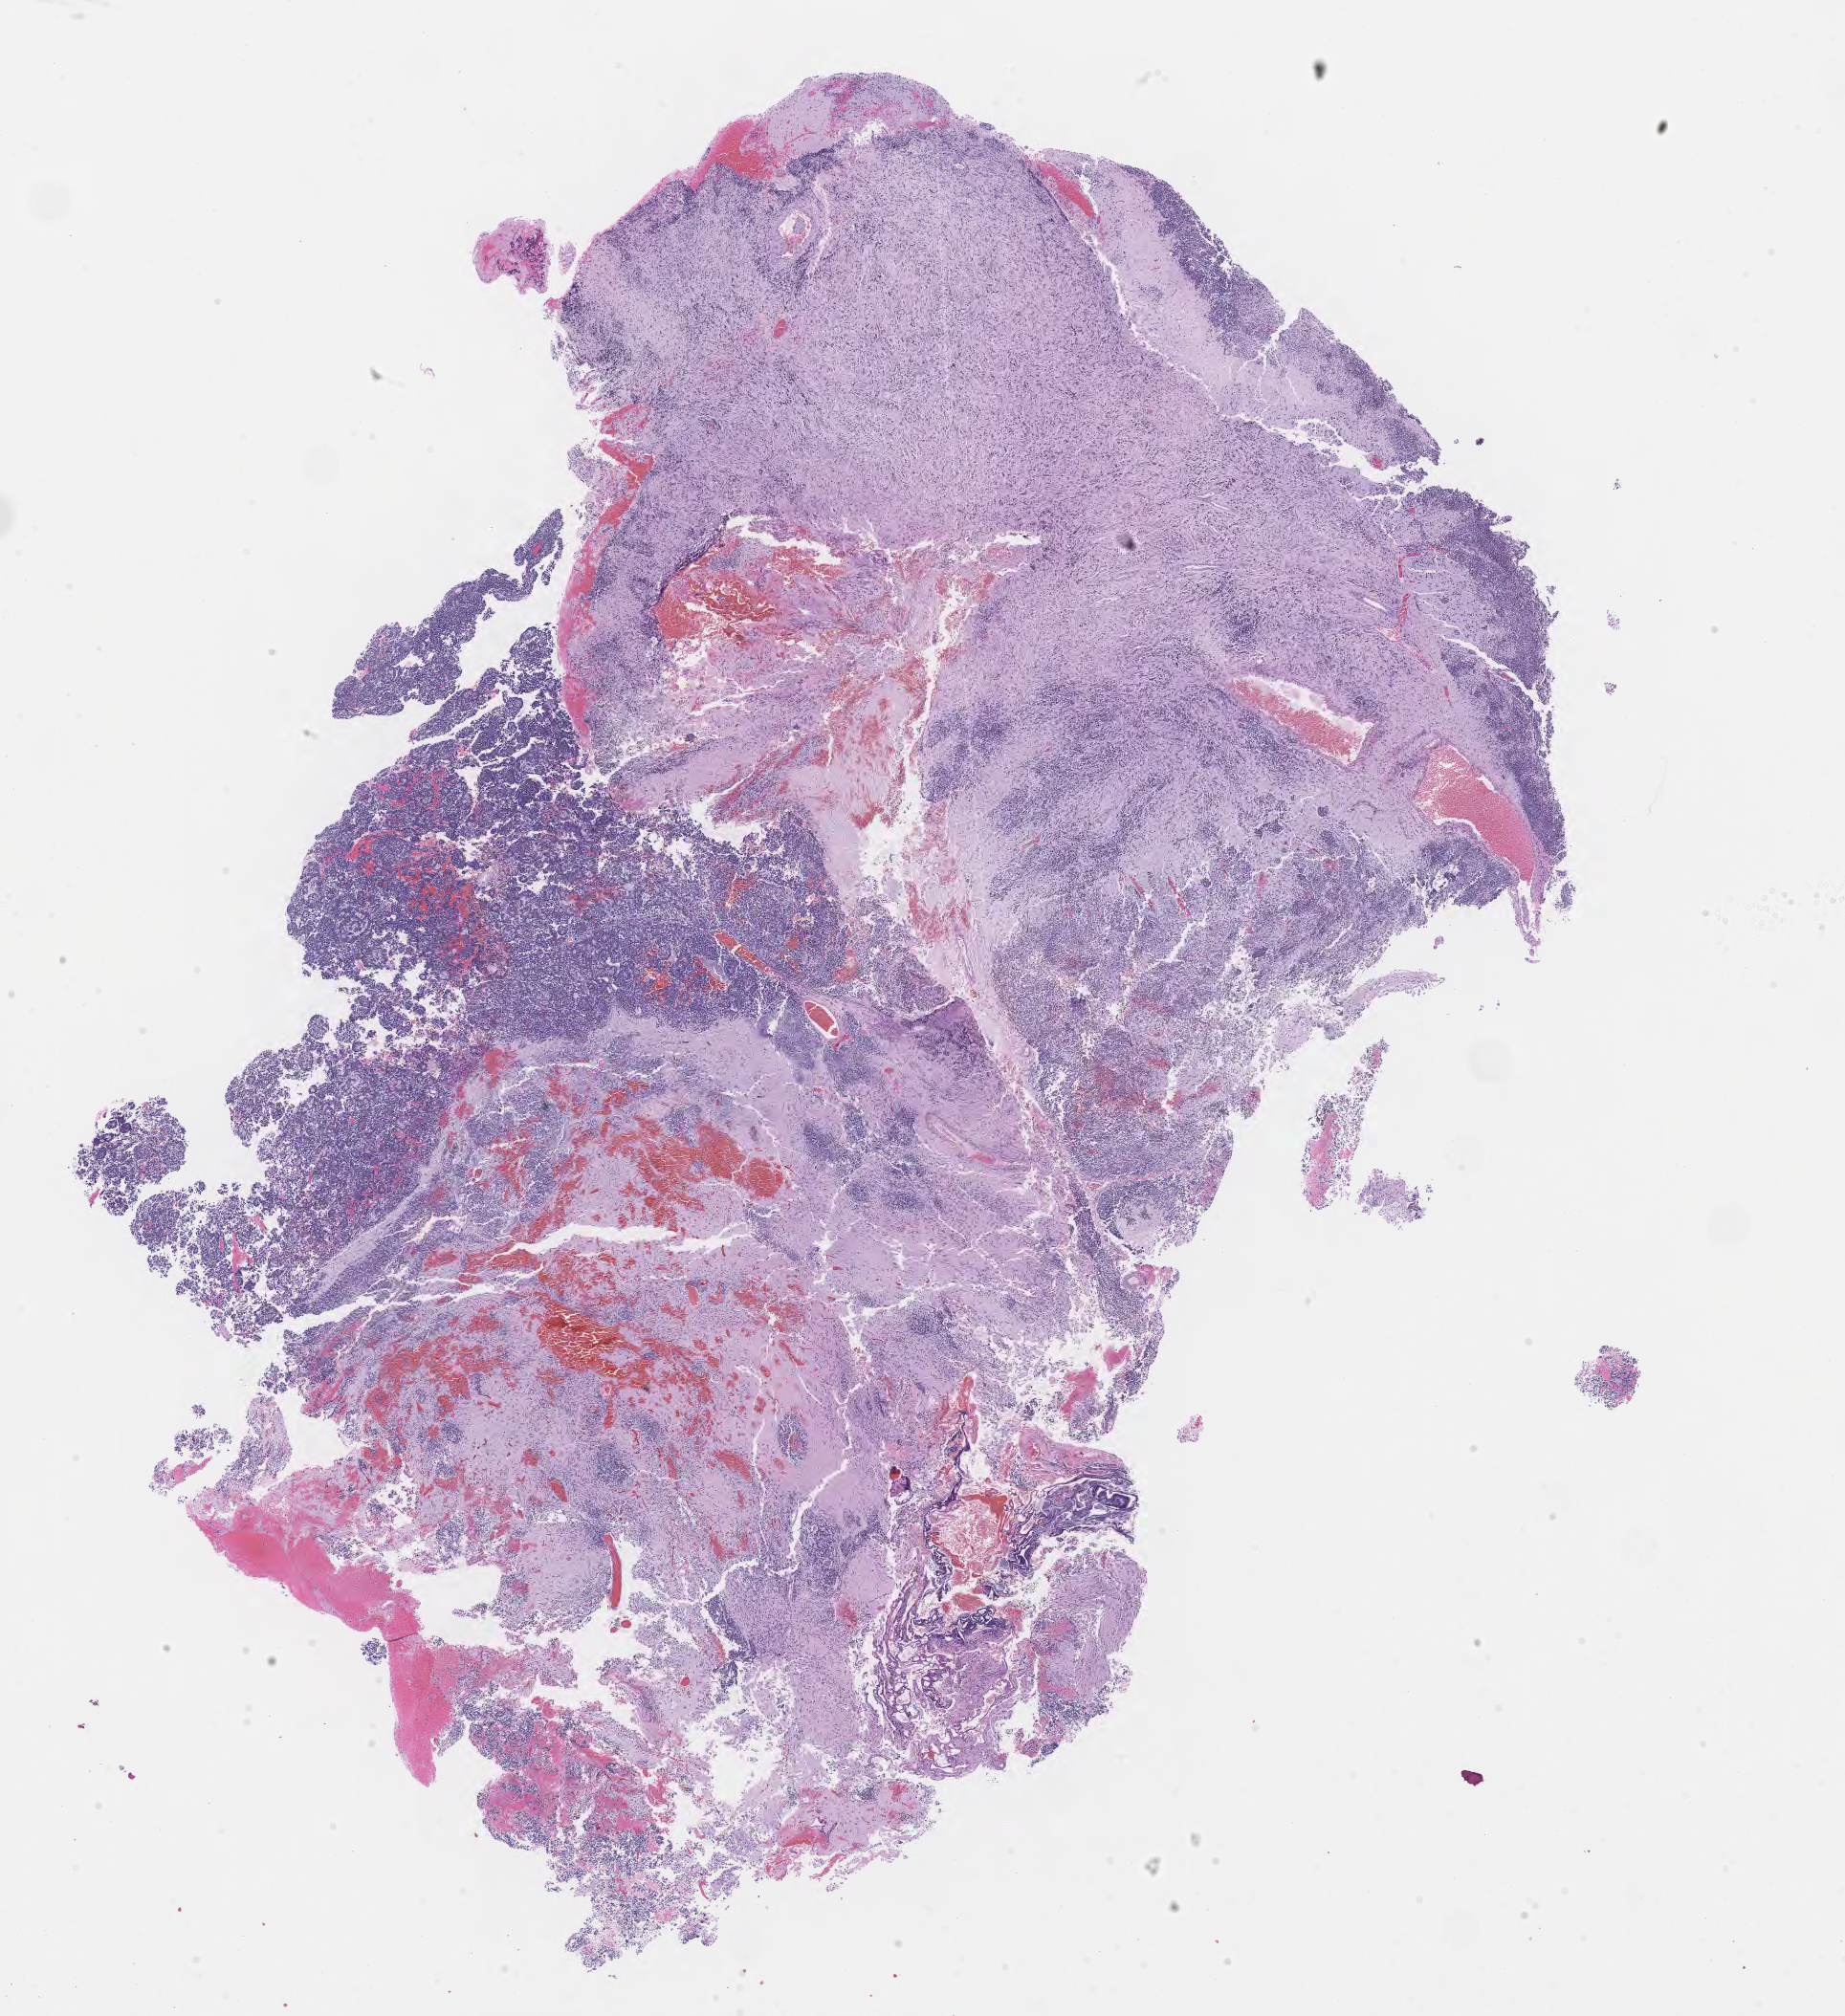
Digitized haematoxylin and eosin-stained section of tumor tissue from the brain — whole scanned area (about 15.6 x 17.0 mm) shown as a low-resolution overview, formalin-fixed, paraffin-embedded (FFPE) tissue. Patient male; age 203 months (16 years 11 months).
Recorded diagnosis: Medulloblastoma, NOS.